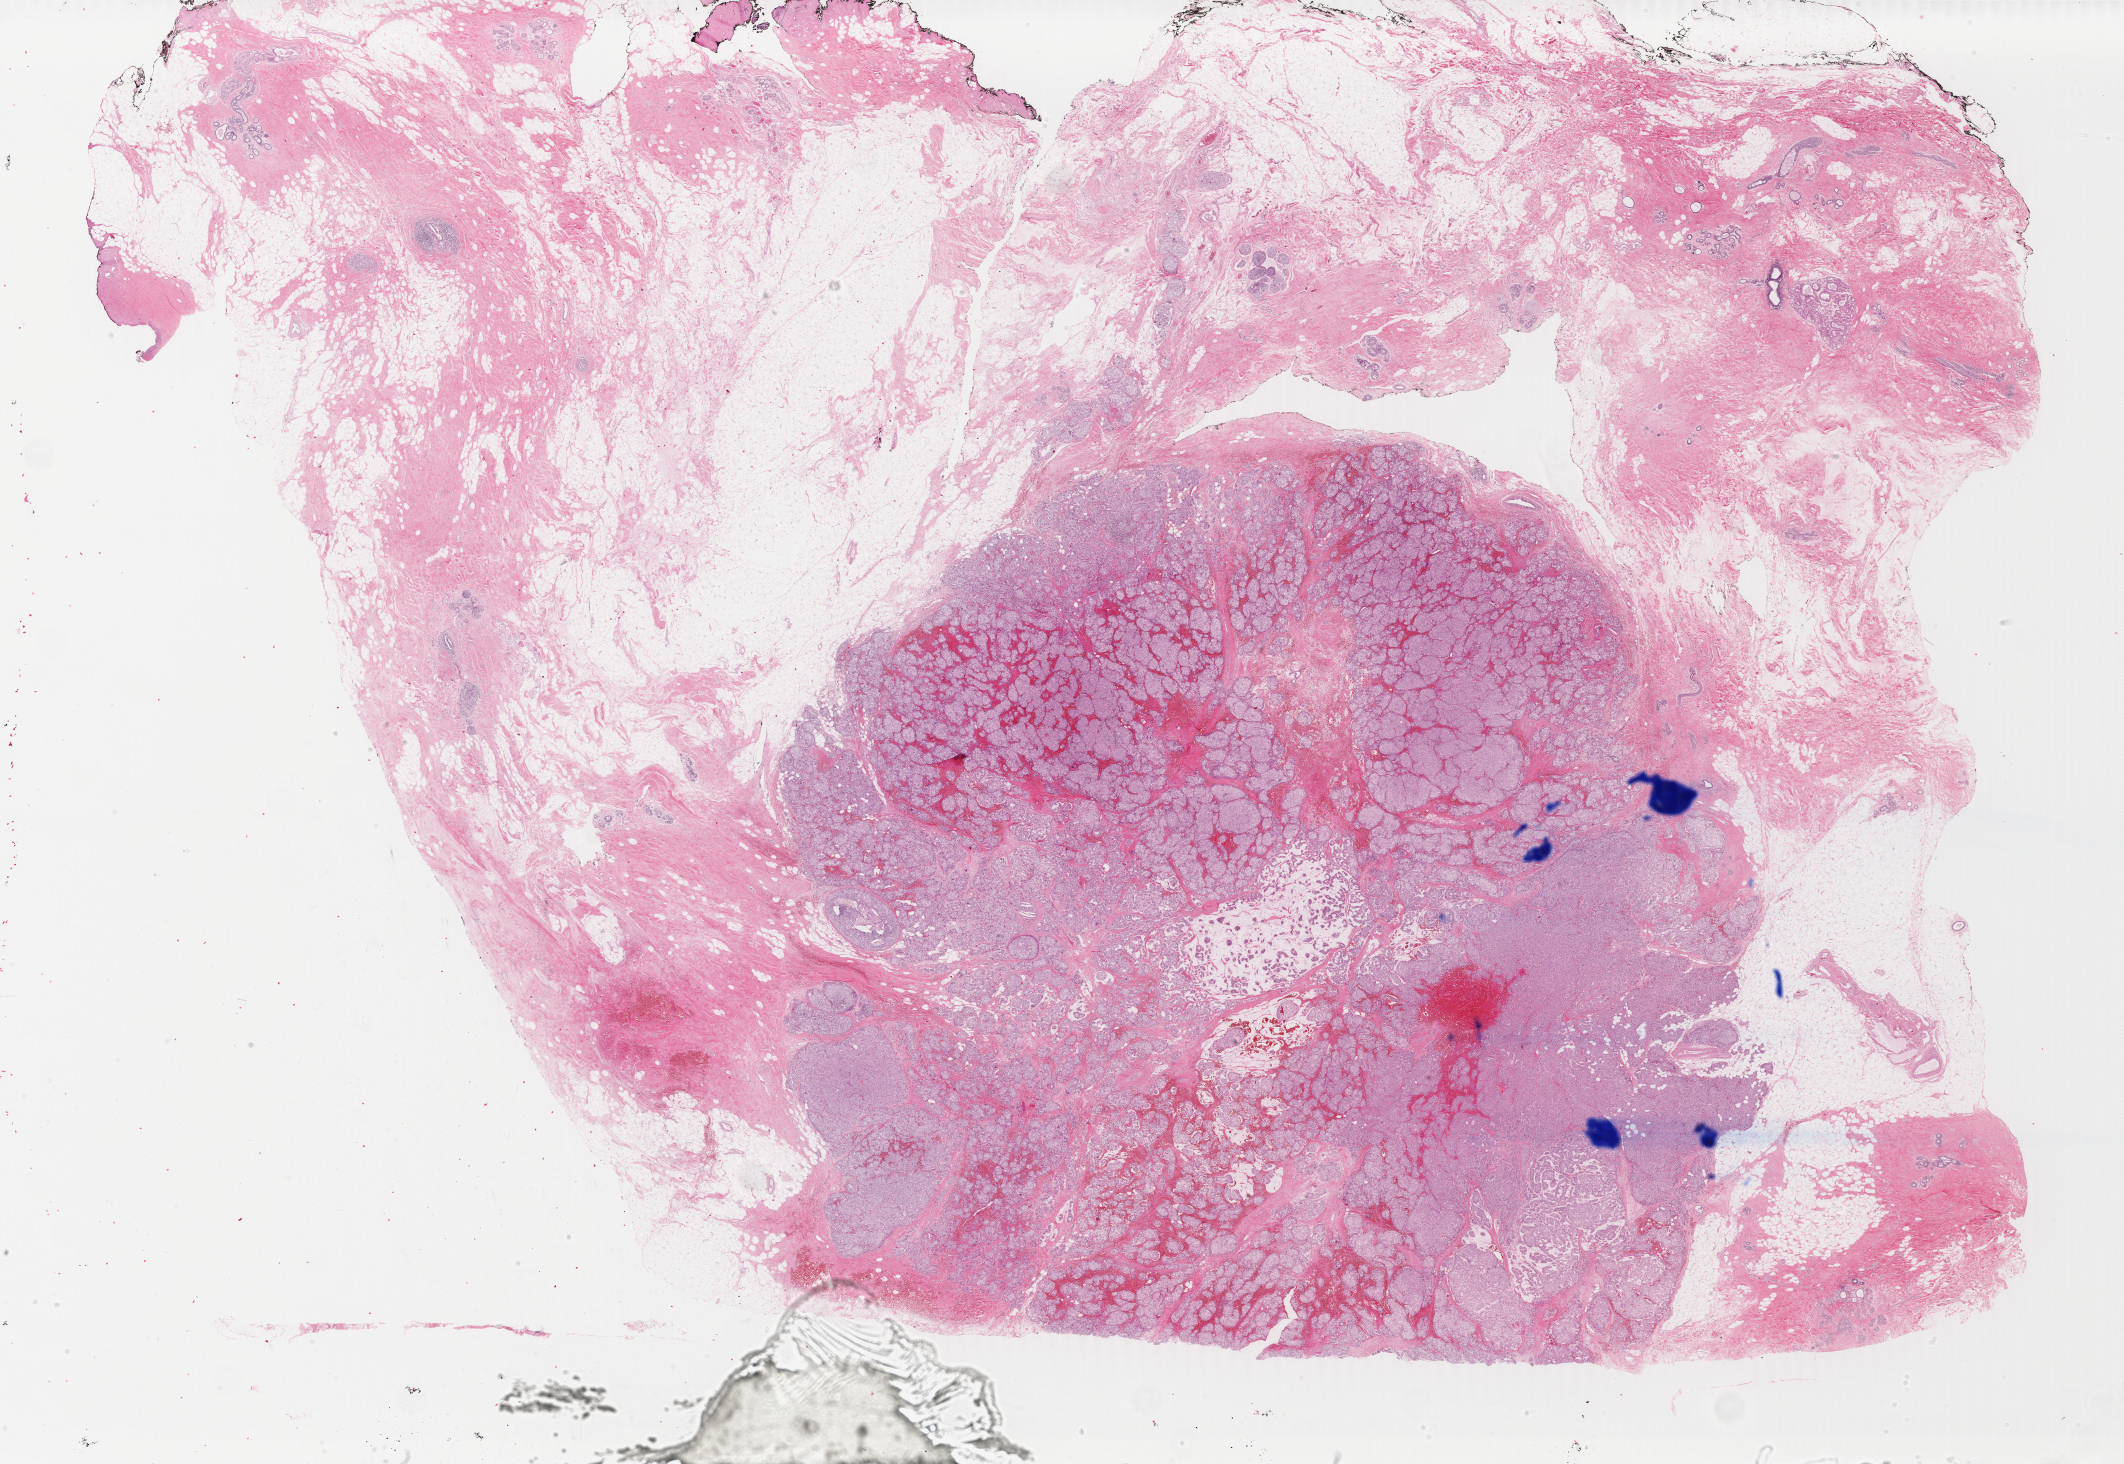
Digitized Hematoxylin and eosin (H&E) stained tissue section (whole slide), whole scanned area (about 33.8 x 23.3 mm) shown as a low-resolution overview, formalin-fixed paraffin-embedded (FFPE) diagnostic section, primary tumour sample from the breast. Patient: female, age at initial diagnosis 45 years.
Laterality: right. Pathologic diagnosis: Infiltrating duct mixed with other types of carcinoma.